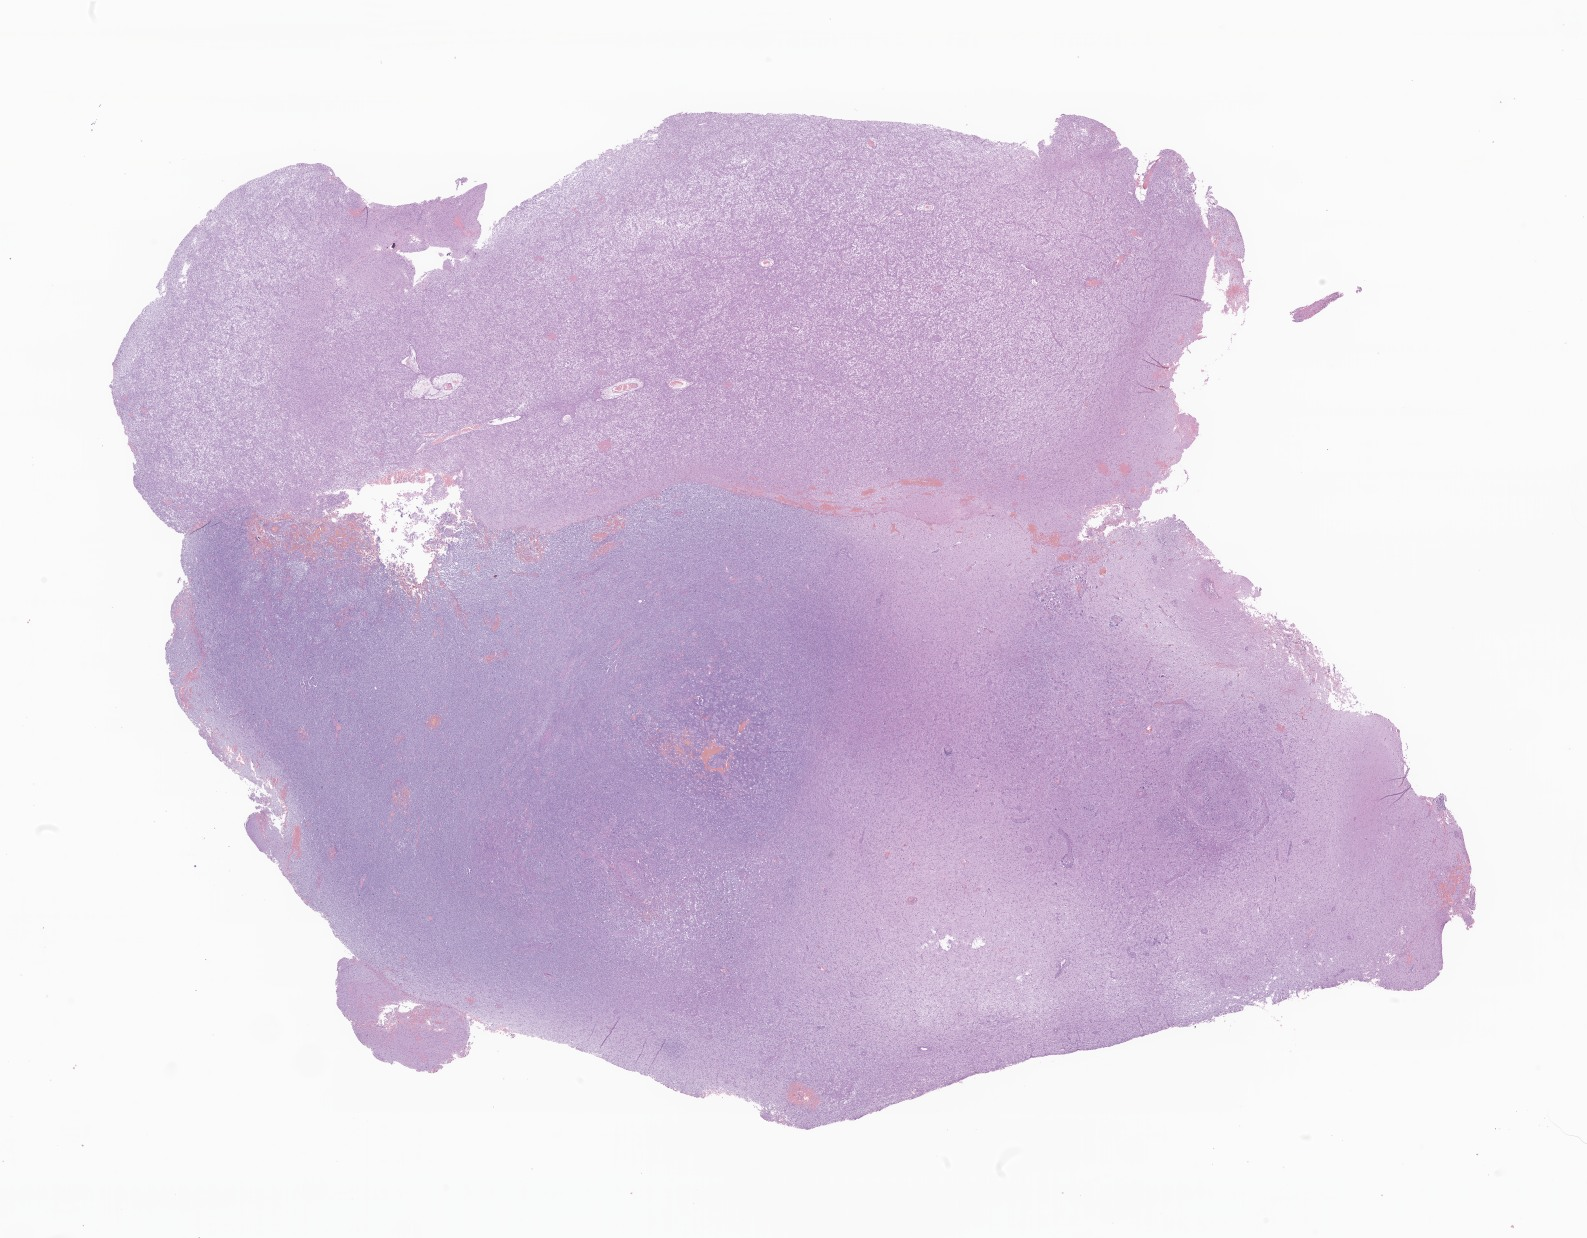
Digitized haematoxylin and eosin-stained section of tumor tissue from the brain — low-resolution overview of the scanned area, about 26.8 x 20.9 mm, formalin-fixed paraffin-embedded section. Male patient, age 97 months (8 years 1 month).
Diagnosis (ICD-O-3 morphology term): Glioma, malignant.